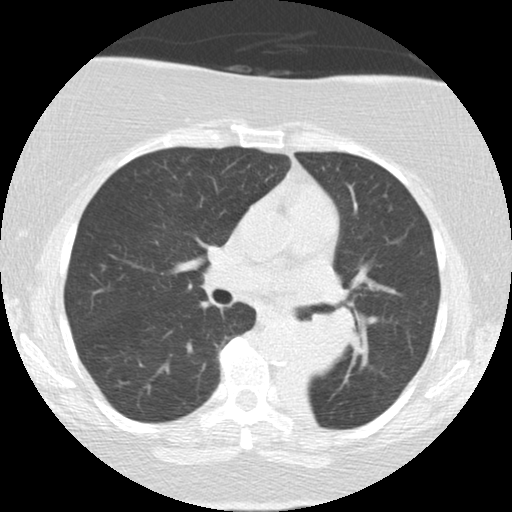
Low-dose screening chest CT, one axial slice; position 78 of 136 along the scan axis; reconstruction kernel STANDARD; 120 kVp; lung window (W 1500 / L -600 HU); 2.5 mm slice thickness; 512 × 512 image matrix, field of view 309 × 309 mm.
Annotated regions visible in this slice (expert manual segmentation):
- lesion 2 (tumor, mediastinum): bounding box [x1, y1, x2, y2] px = [300, 273, 356, 372]